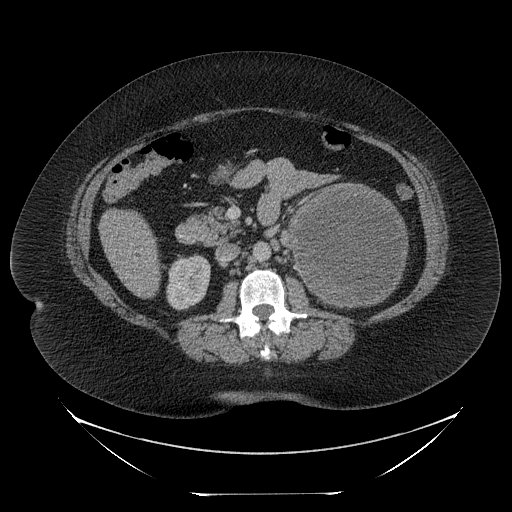
Contrast-enhanced abdominal CT, one axial slice. Slice 125 of 205 in the series (ordered by position). Reconstruction kernel STANDARD. Intravenous contrast given. Soft-tissue window (W 400 / L 40 HU). 2.5 mm slice thickness. 512 × 512 image matrix, field of view 500 × 500 mm. Female patient, age 53 years. Case-level facts recorded for this patient, not image findings: diagnosis: adrenocortical carcinoma; tumour side: left adrenal; tumour size at pathology: 17 cm; Ki-67 index: 20 %; stage (as recorded): 3.
Structures marked on this image (semi-automatic segmentation, software-assisted and operator-edited):
- mass: bounding box (x1, y1, x2, y2) in pixels: (293, 187, 406, 305)